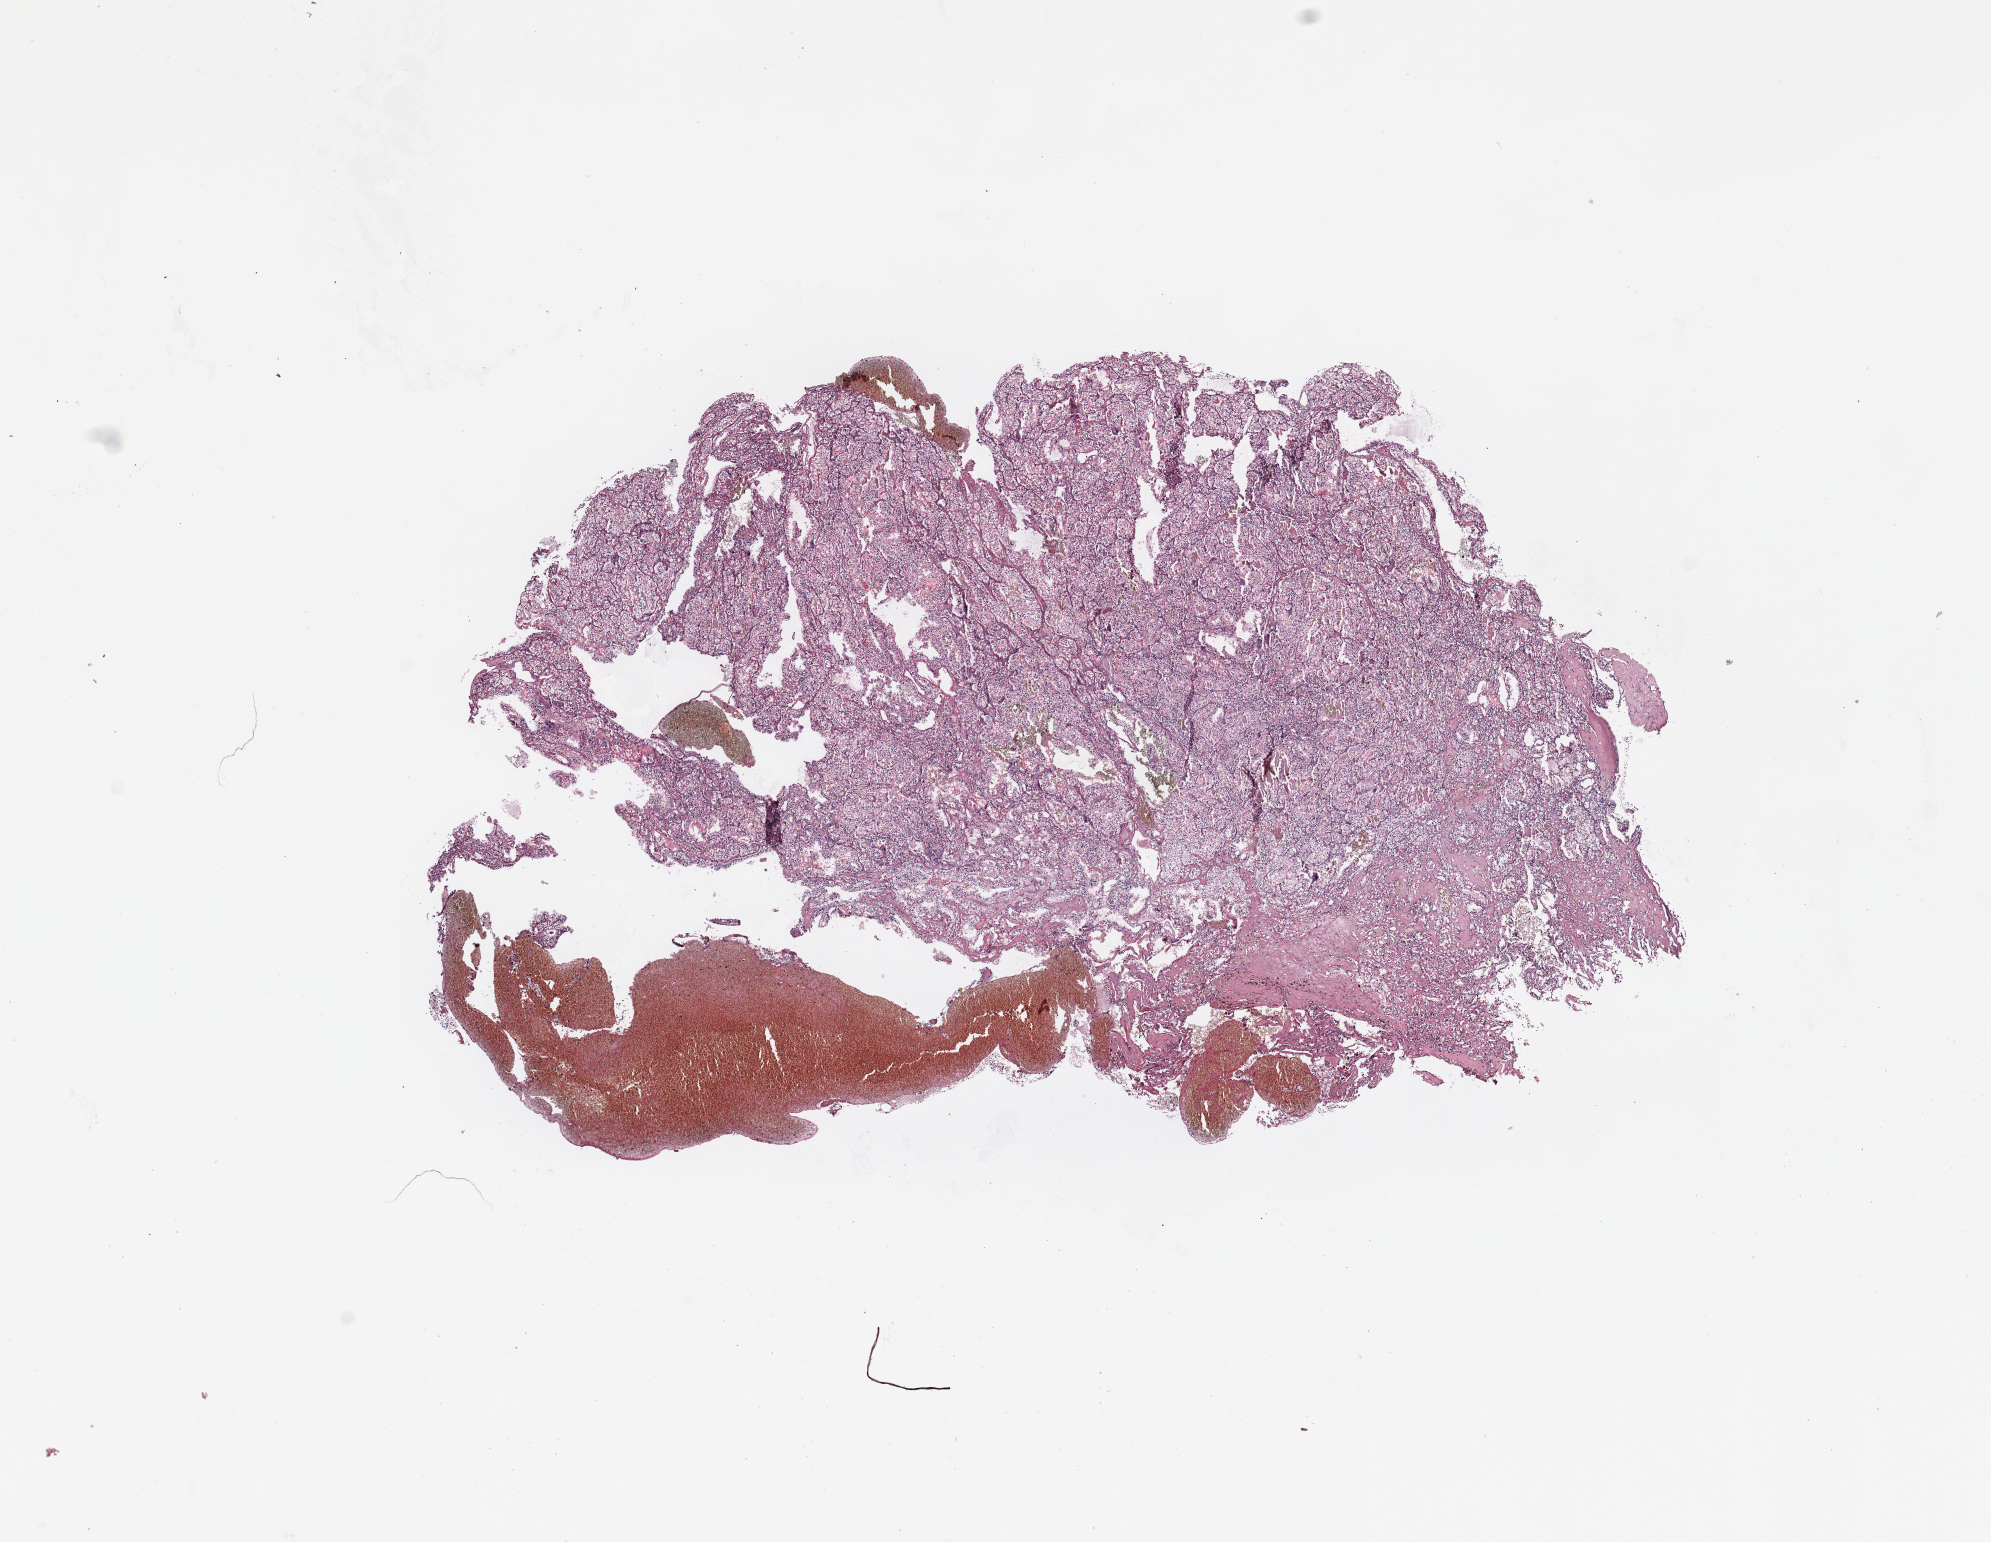
H&E whole-slide image — whole scanned area (about 15.8 x 12.2 mm, acquisition: 20x scan) shown as a low-resolution overview; tumour tissue sample, sampled site: kidney. Male, 61 y/o. Histologic grade: G3 (poorly differentiated). Pathologist review of this section (percent, as recorded): tumour nuclei 90%, necrosis 0%.
Primary tumour site (as recorded): upper pole. AJCC pathologic stage: II. Diagnosis: Renal cell carcinoma, NOS.